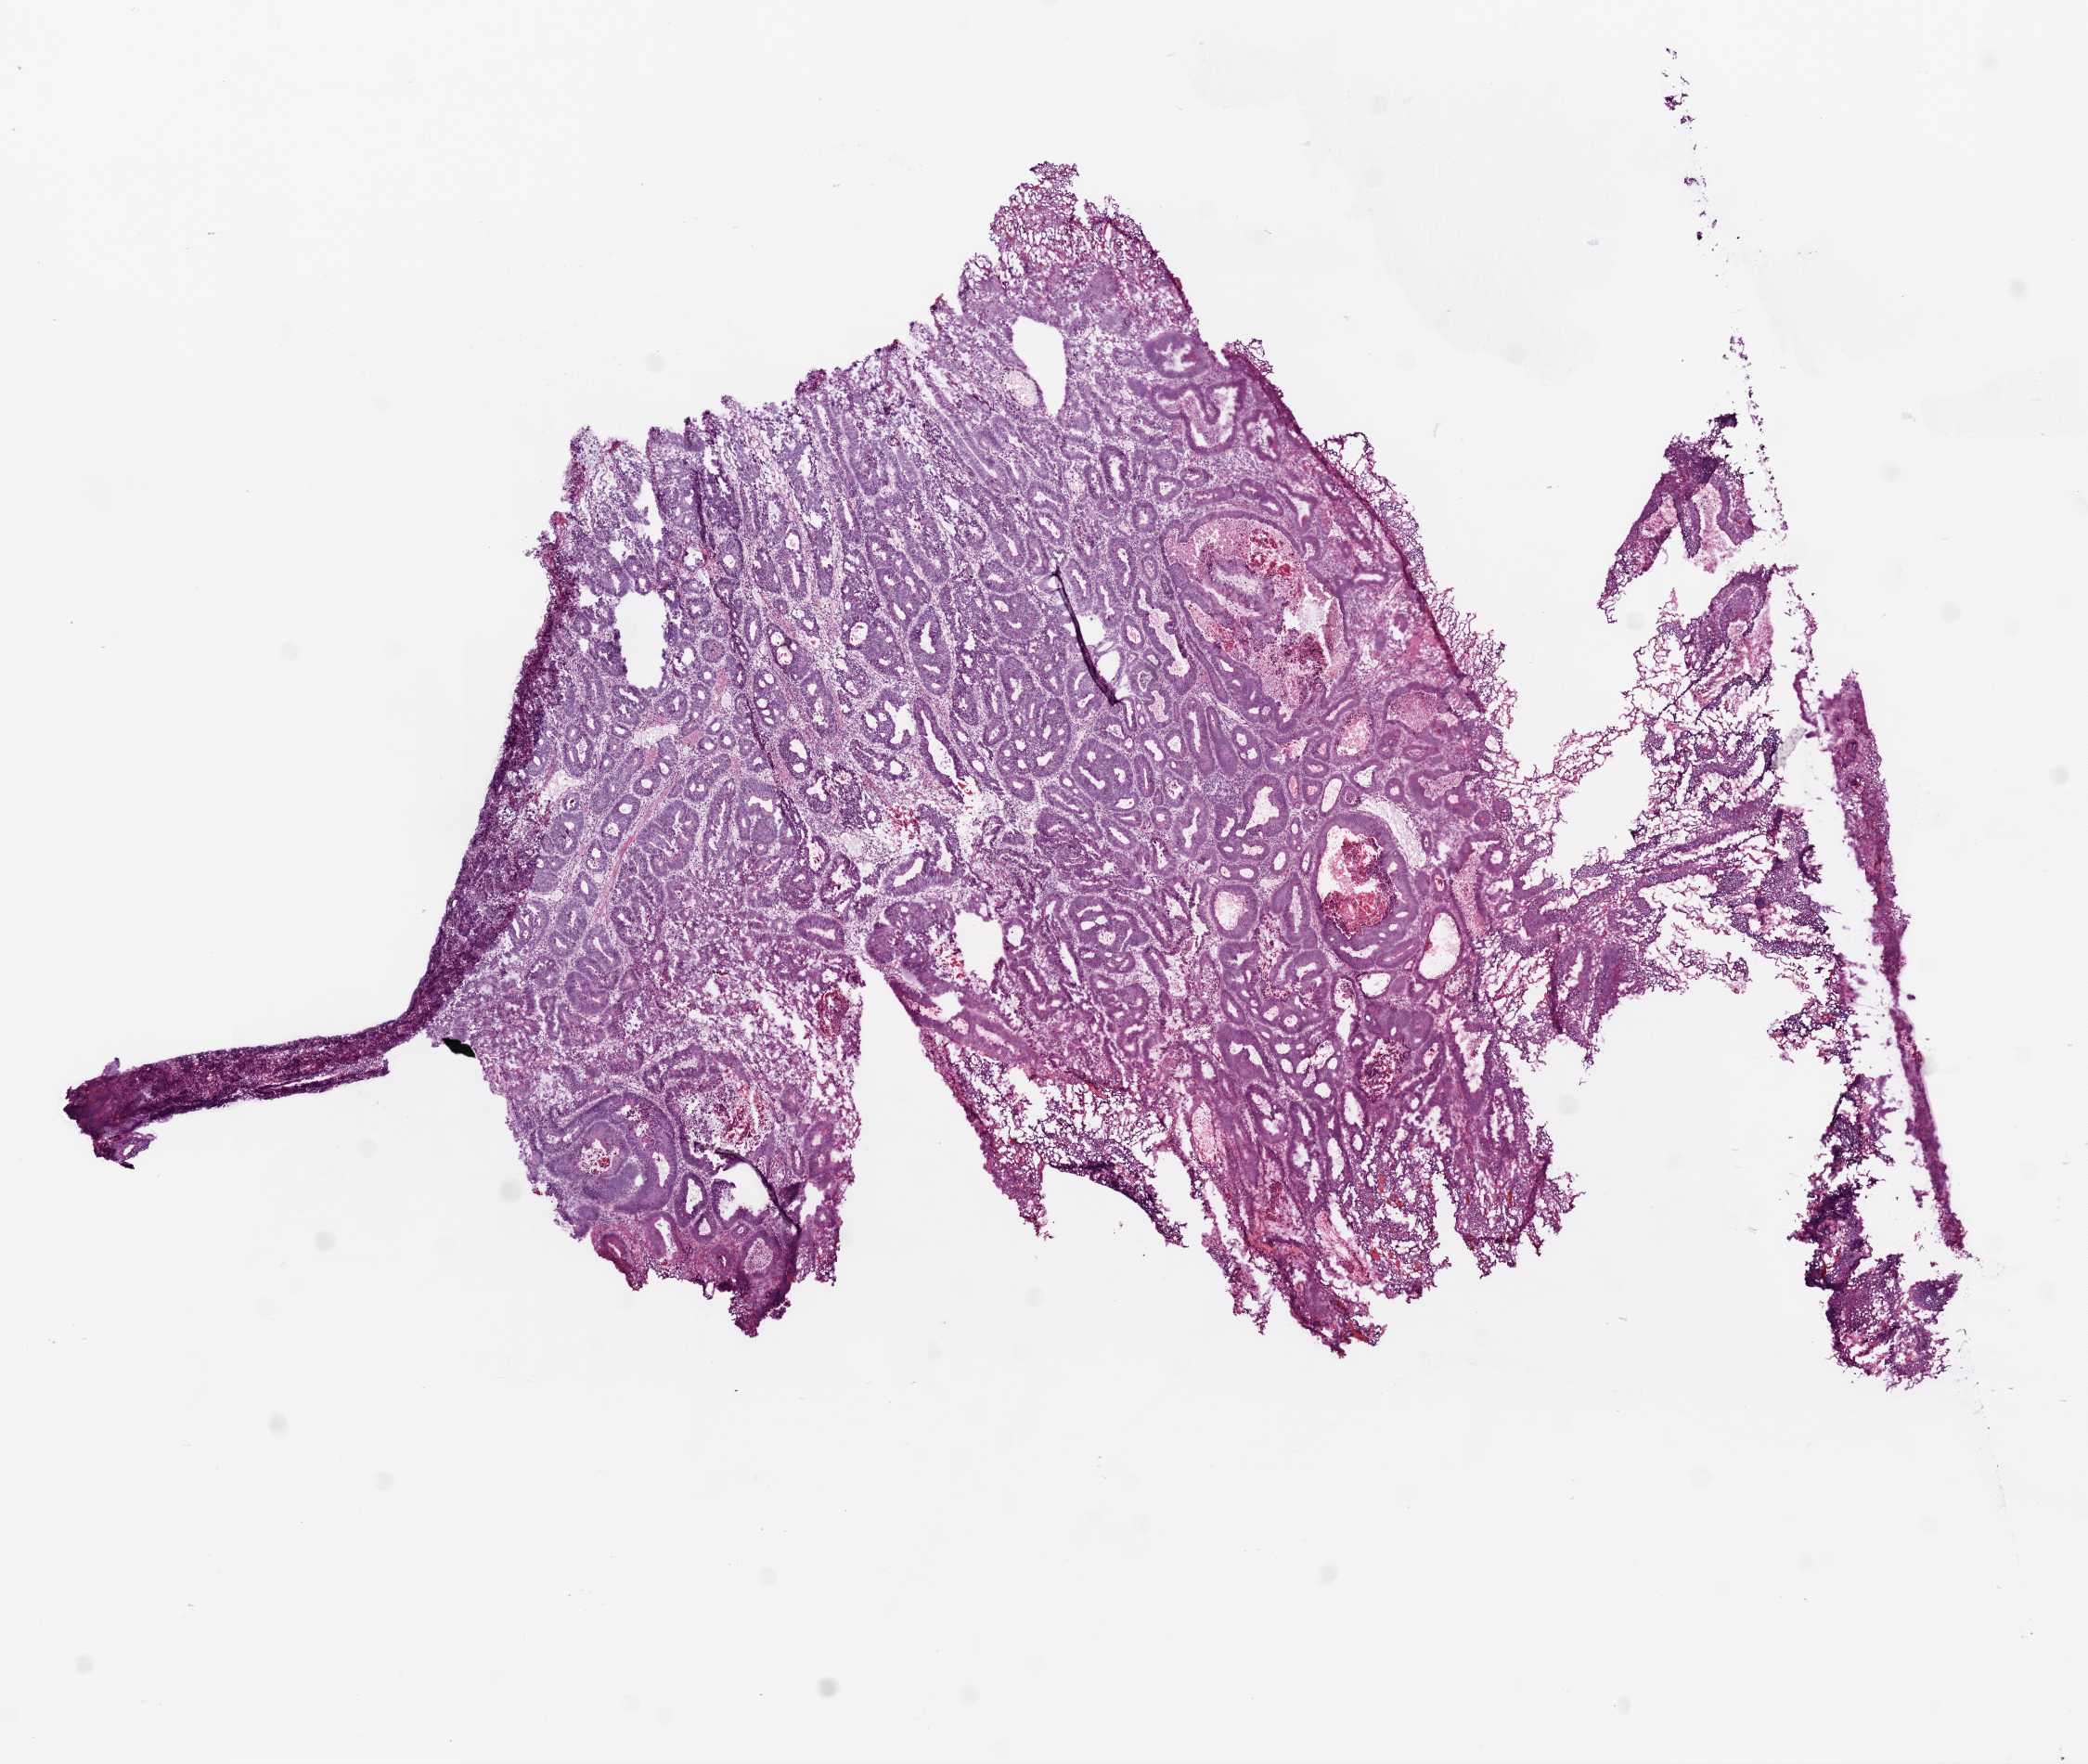
Whole-slide histology image, H&E-stained, a low-resolution overview of the entire scanned area, about 9.0 x 7.6 mm. Frozen section. Primary tumour sample from the rectum. Patient: female, age at initial diagnosis 66 years.
Histologic diagnosis: Adenocarcinoma, NOS (colon, NOS).